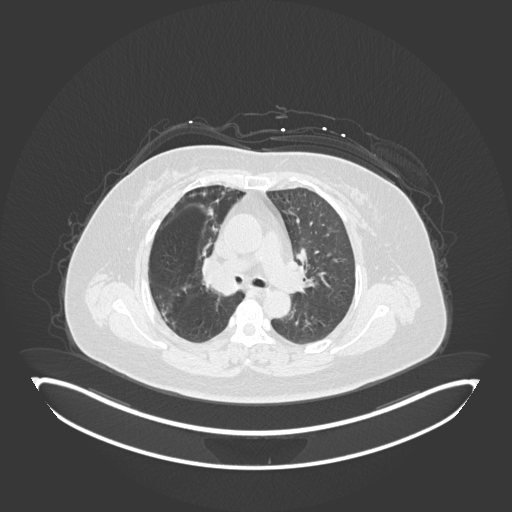
Chest CT, one axial slice; reconstruction kernel B30f; 120 kVp; lung window (W 1500 / L -600 HU); 1 mm slice thickness; 512 × 512 image matrix. Patient: female, 60 years. Case-level facts recorded for this patient, not image findings: clinical TNM (as recorded): T1c N0 M0.
Annotated regions visible in this slice (bounding box drawn by a radiologist):
- lung tumour (recorded histology: squamous cell carcinoma): box from (x=195, y=255) to (x=244, y=300) px